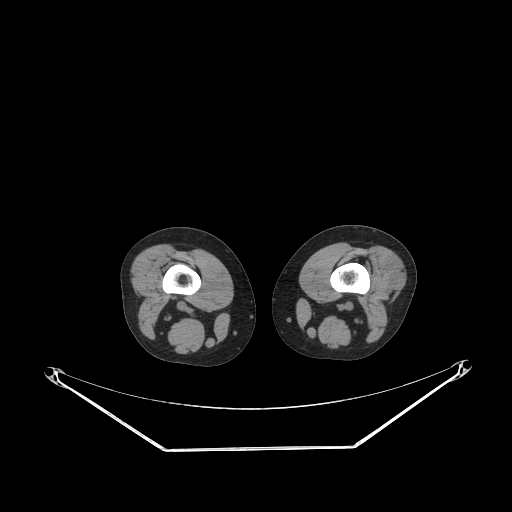
CT of an extremity soft-tissue mass (from a PET/CT study), one axial slice. Slice 179 of 223 in the series (ordered by position). Reconstruction kernel STANDARD. 140 kVp. Soft-tissue window (W 400 / L 40 HU). 512 × 512 image matrix. Female patient. From the clinical record (not read from this slice): histological type: spindle cell suggestive of biphasic synovial sarcoma; grade: intermediate; site of the primary tumour: left knee.
Outlined on this slice (expert contour drawn on MRI and transferred to this co-registered scan by the dataset authors):
- gross tumour volume including surrounding oedema: box from (x=379, y=247) to (x=405, y=293) px
- gross tumour volume (mass): (x=379, y=247)–(x=405, y=293)